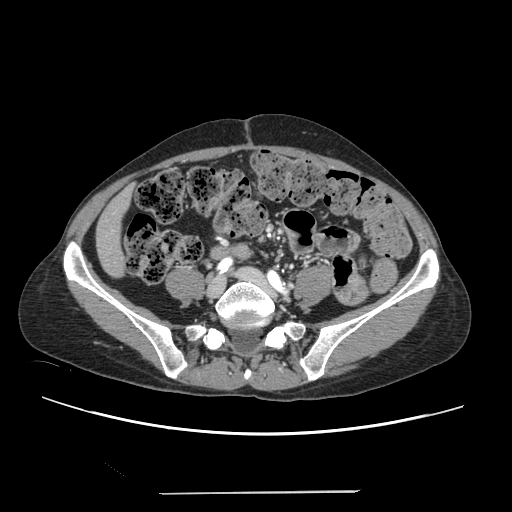
Contrast-enhanced abdominal CT, one axial slice. Position 19 of 240 along the scan axis. 120 kVp. Intravenous contrast given. Soft-tissue window (W 400 / L 40 HU). 1.25 mm slice thickness. 512 × 512 image matrix, field of view 371 × 371 mm. Female patient, age 60 years. Case-level facts recorded for this patient, not image findings: diagnosis: colorectal cancer liver metastases, imaged before liver resection; multiple liver metastases: no; largest metastasis: 1.5 cm; disease in both lobes: no.
Structures marked on this image (manually delineated by an expert):
- liver: bounding box [x1, y1, x2, y2] px = [97, 190, 132, 276]
- planned liver remnant (the part of the liver to remain after resection): [97, 190, 132, 276]